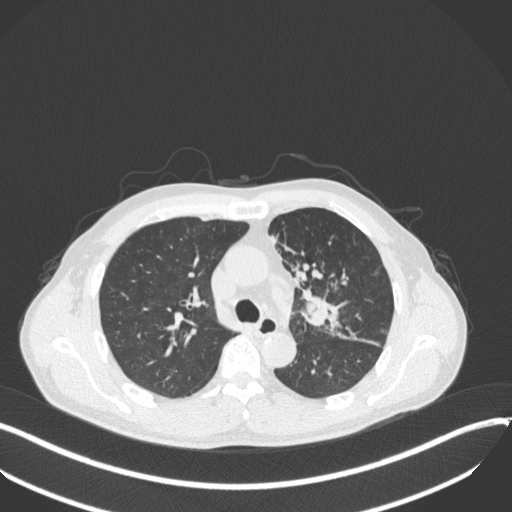
Chest CT, one axial slice; slice 231 of 411 in the series (ordered by position); reconstruction kernel B31f; lung window (W 1500 / L -600 HU); 1 mm slice thickness; 512 × 512 image matrix, field of view 400 × 400 mm. Male patient, age 56 years. Case-level facts recorded for this patient, not image findings: clinical TNM (as recorded): T2a N0 M0.
Structures marked on this image (bounding box drawn by a radiologist):
- lung tumour (recorded histology: squamous cell carcinoma): bounding box (x1, y1, x2, y2) in pixels: (298, 282, 344, 336)